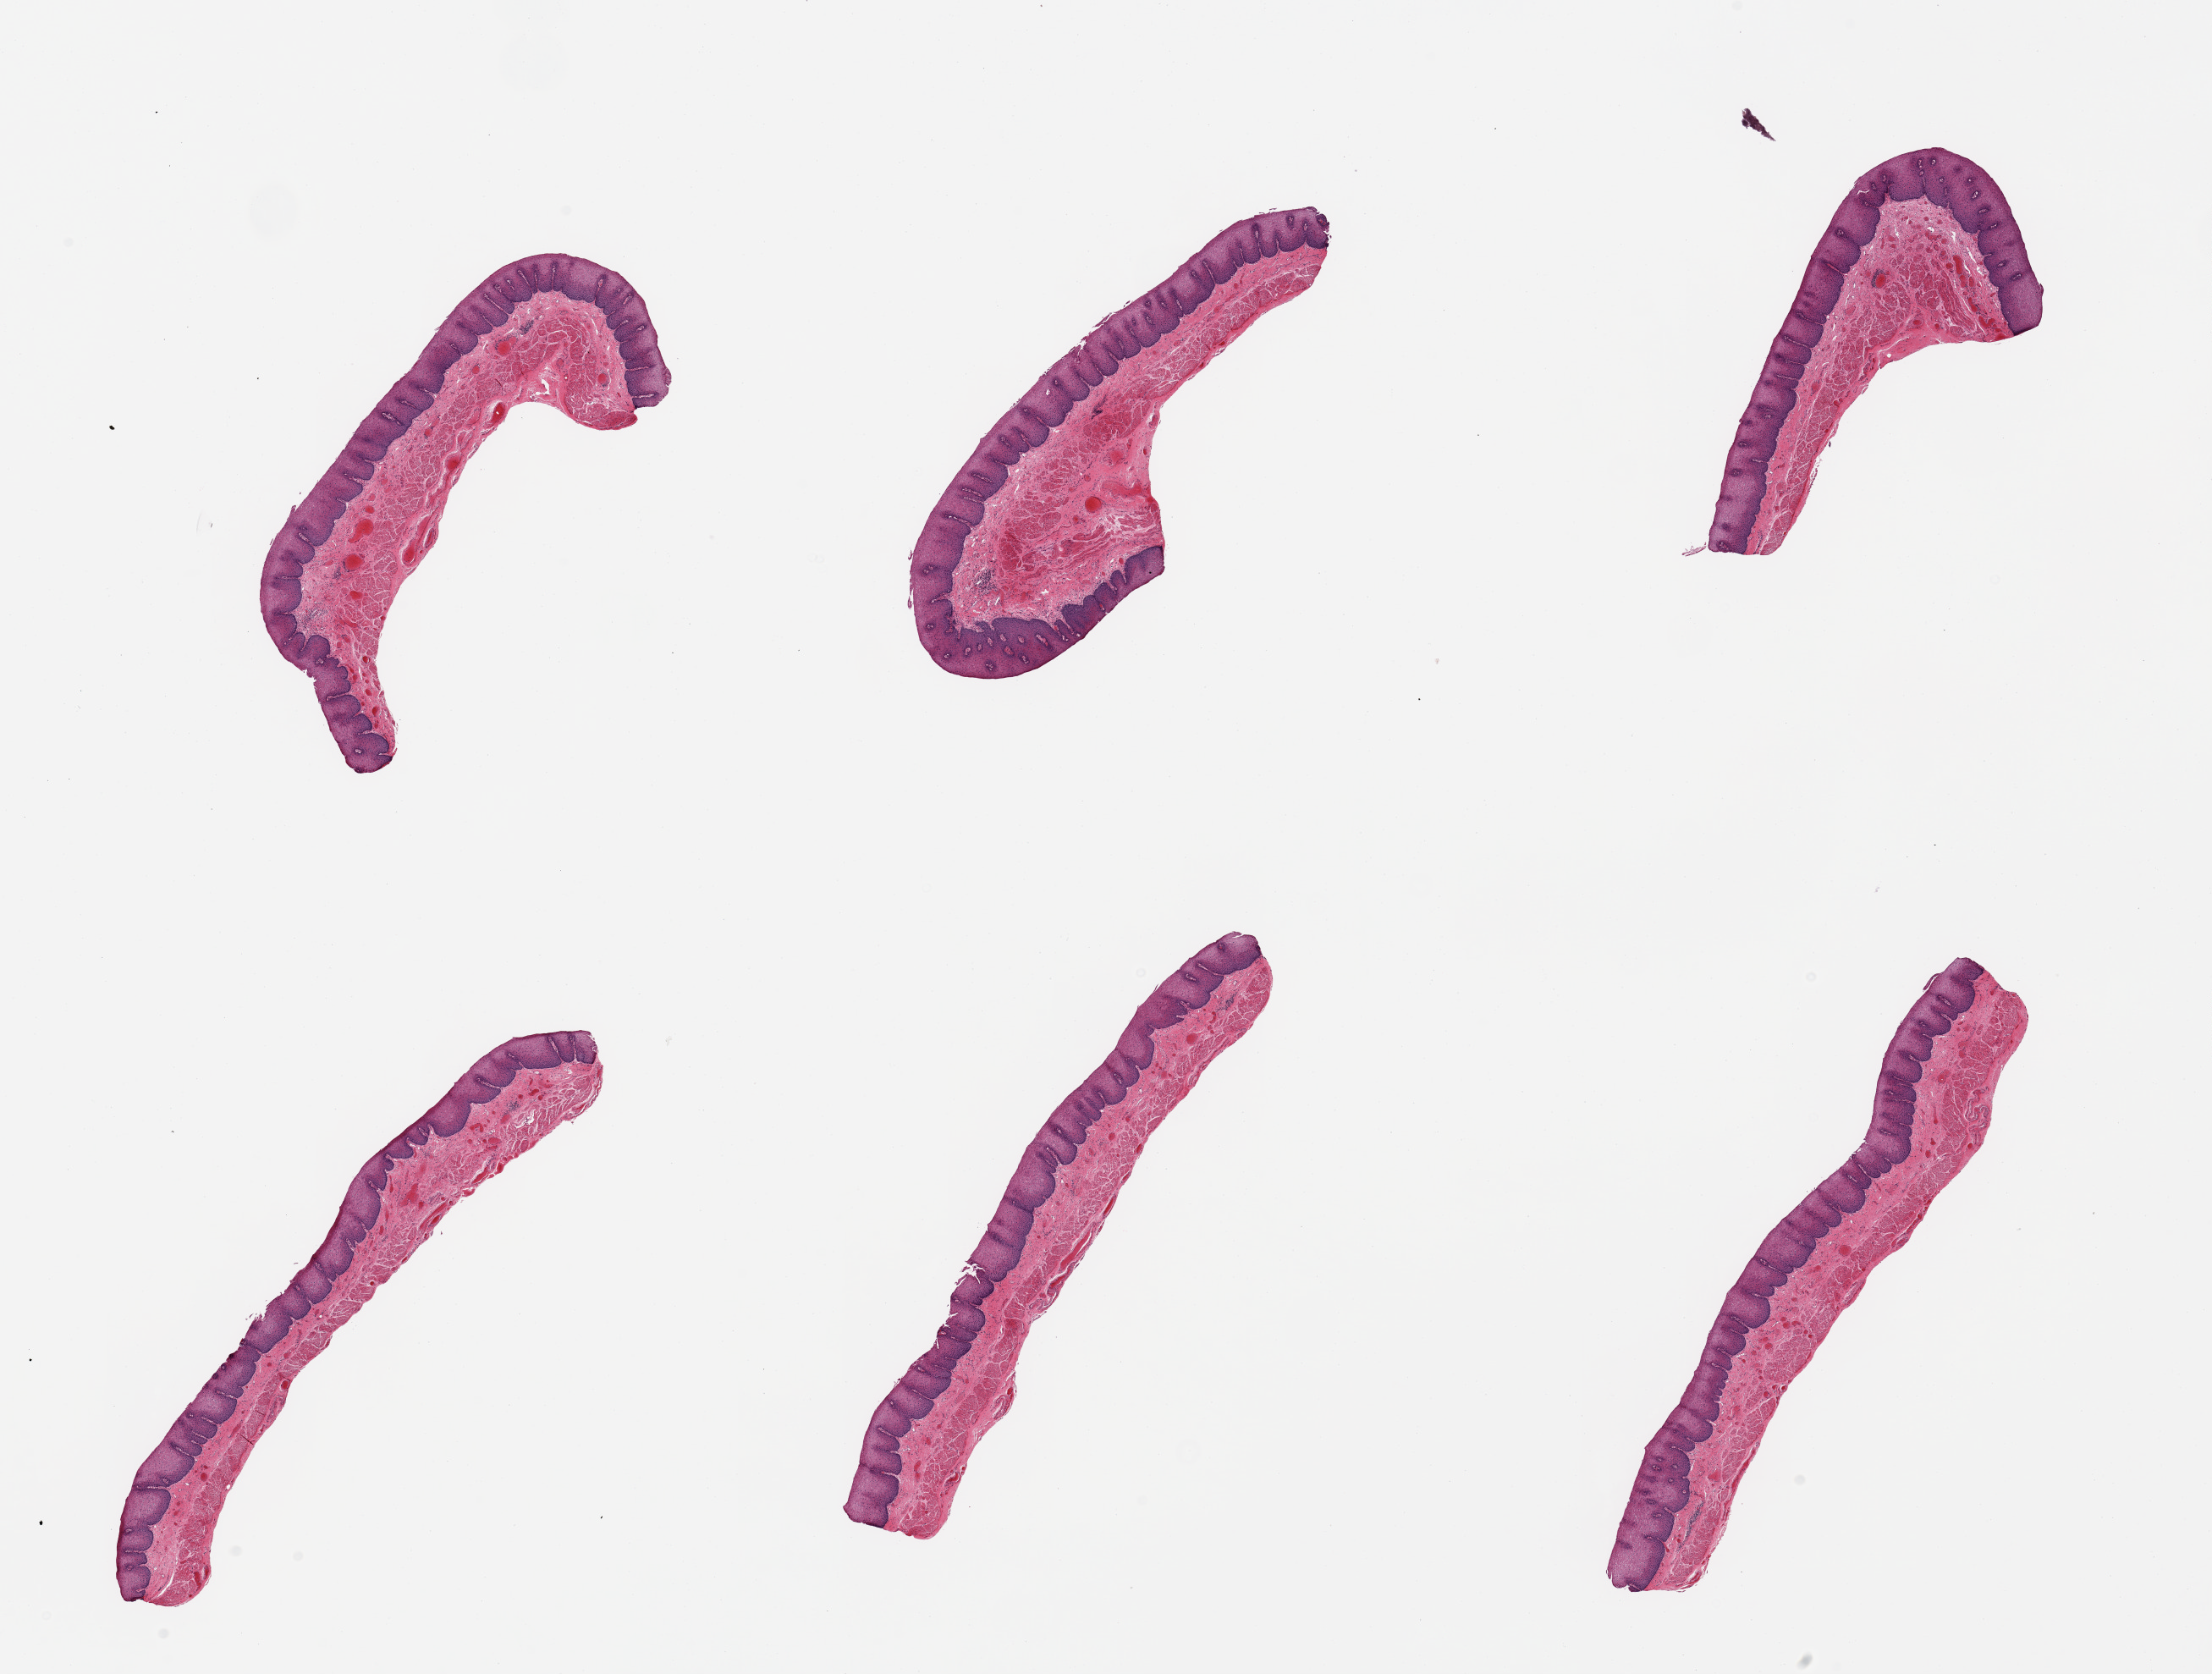
Whole-slide image, H&E stain, brightfield — shown as a low-resolution overview of the whole scanned area (about 20.7 x 15.6 mm, slide scanned at 20x), PAXgene-fixed paraffin-embedded (PFPE) section, section of esophageal mucous membrane (target tissue), tissue donor sample. Donor: female.
Review note (as recorded): 6 pieces; well dissected.